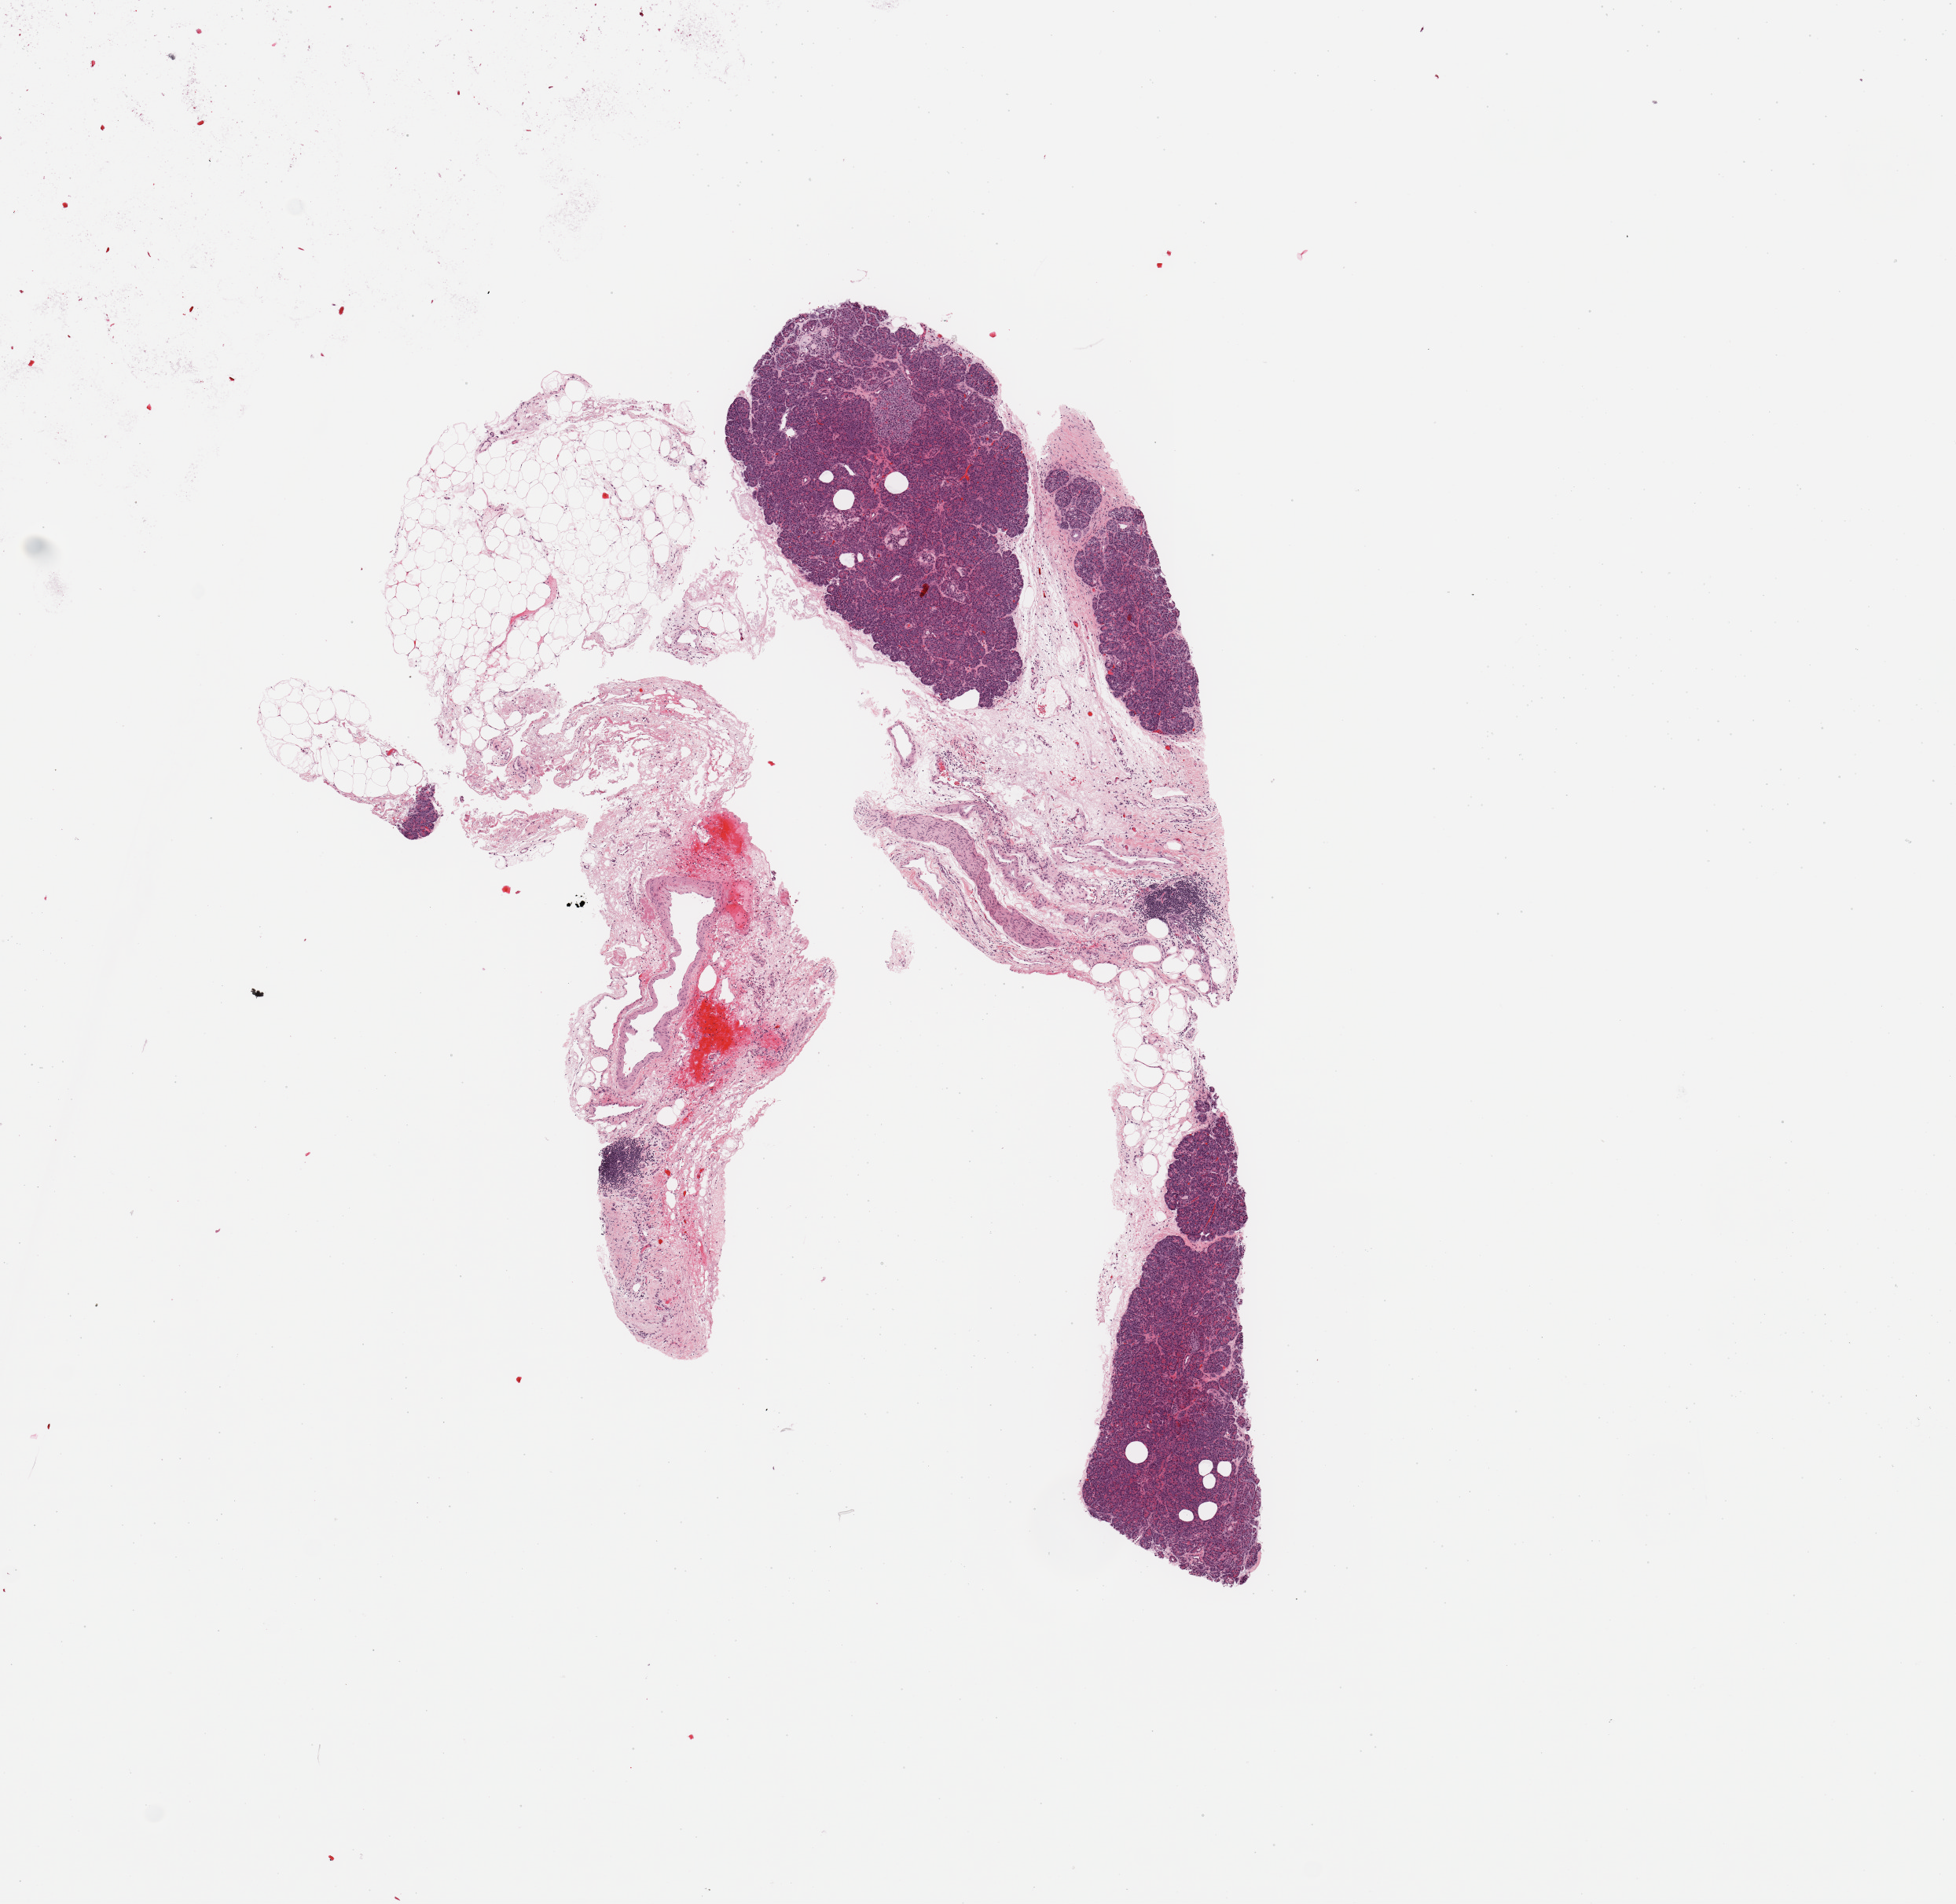
Digitized H&E-stained tissue section (whole slide) — whole scanned area (about 9.8 x 9.6 mm) shown as a low-resolution overview. Normal (non-tumour) tissue sample, sampled site: pancreas. 73-year-old female patient.
* this section: normal (non-tumour) tissue from the same patient
* patient diagnosis: Infiltrating duct carcinoma, NOS